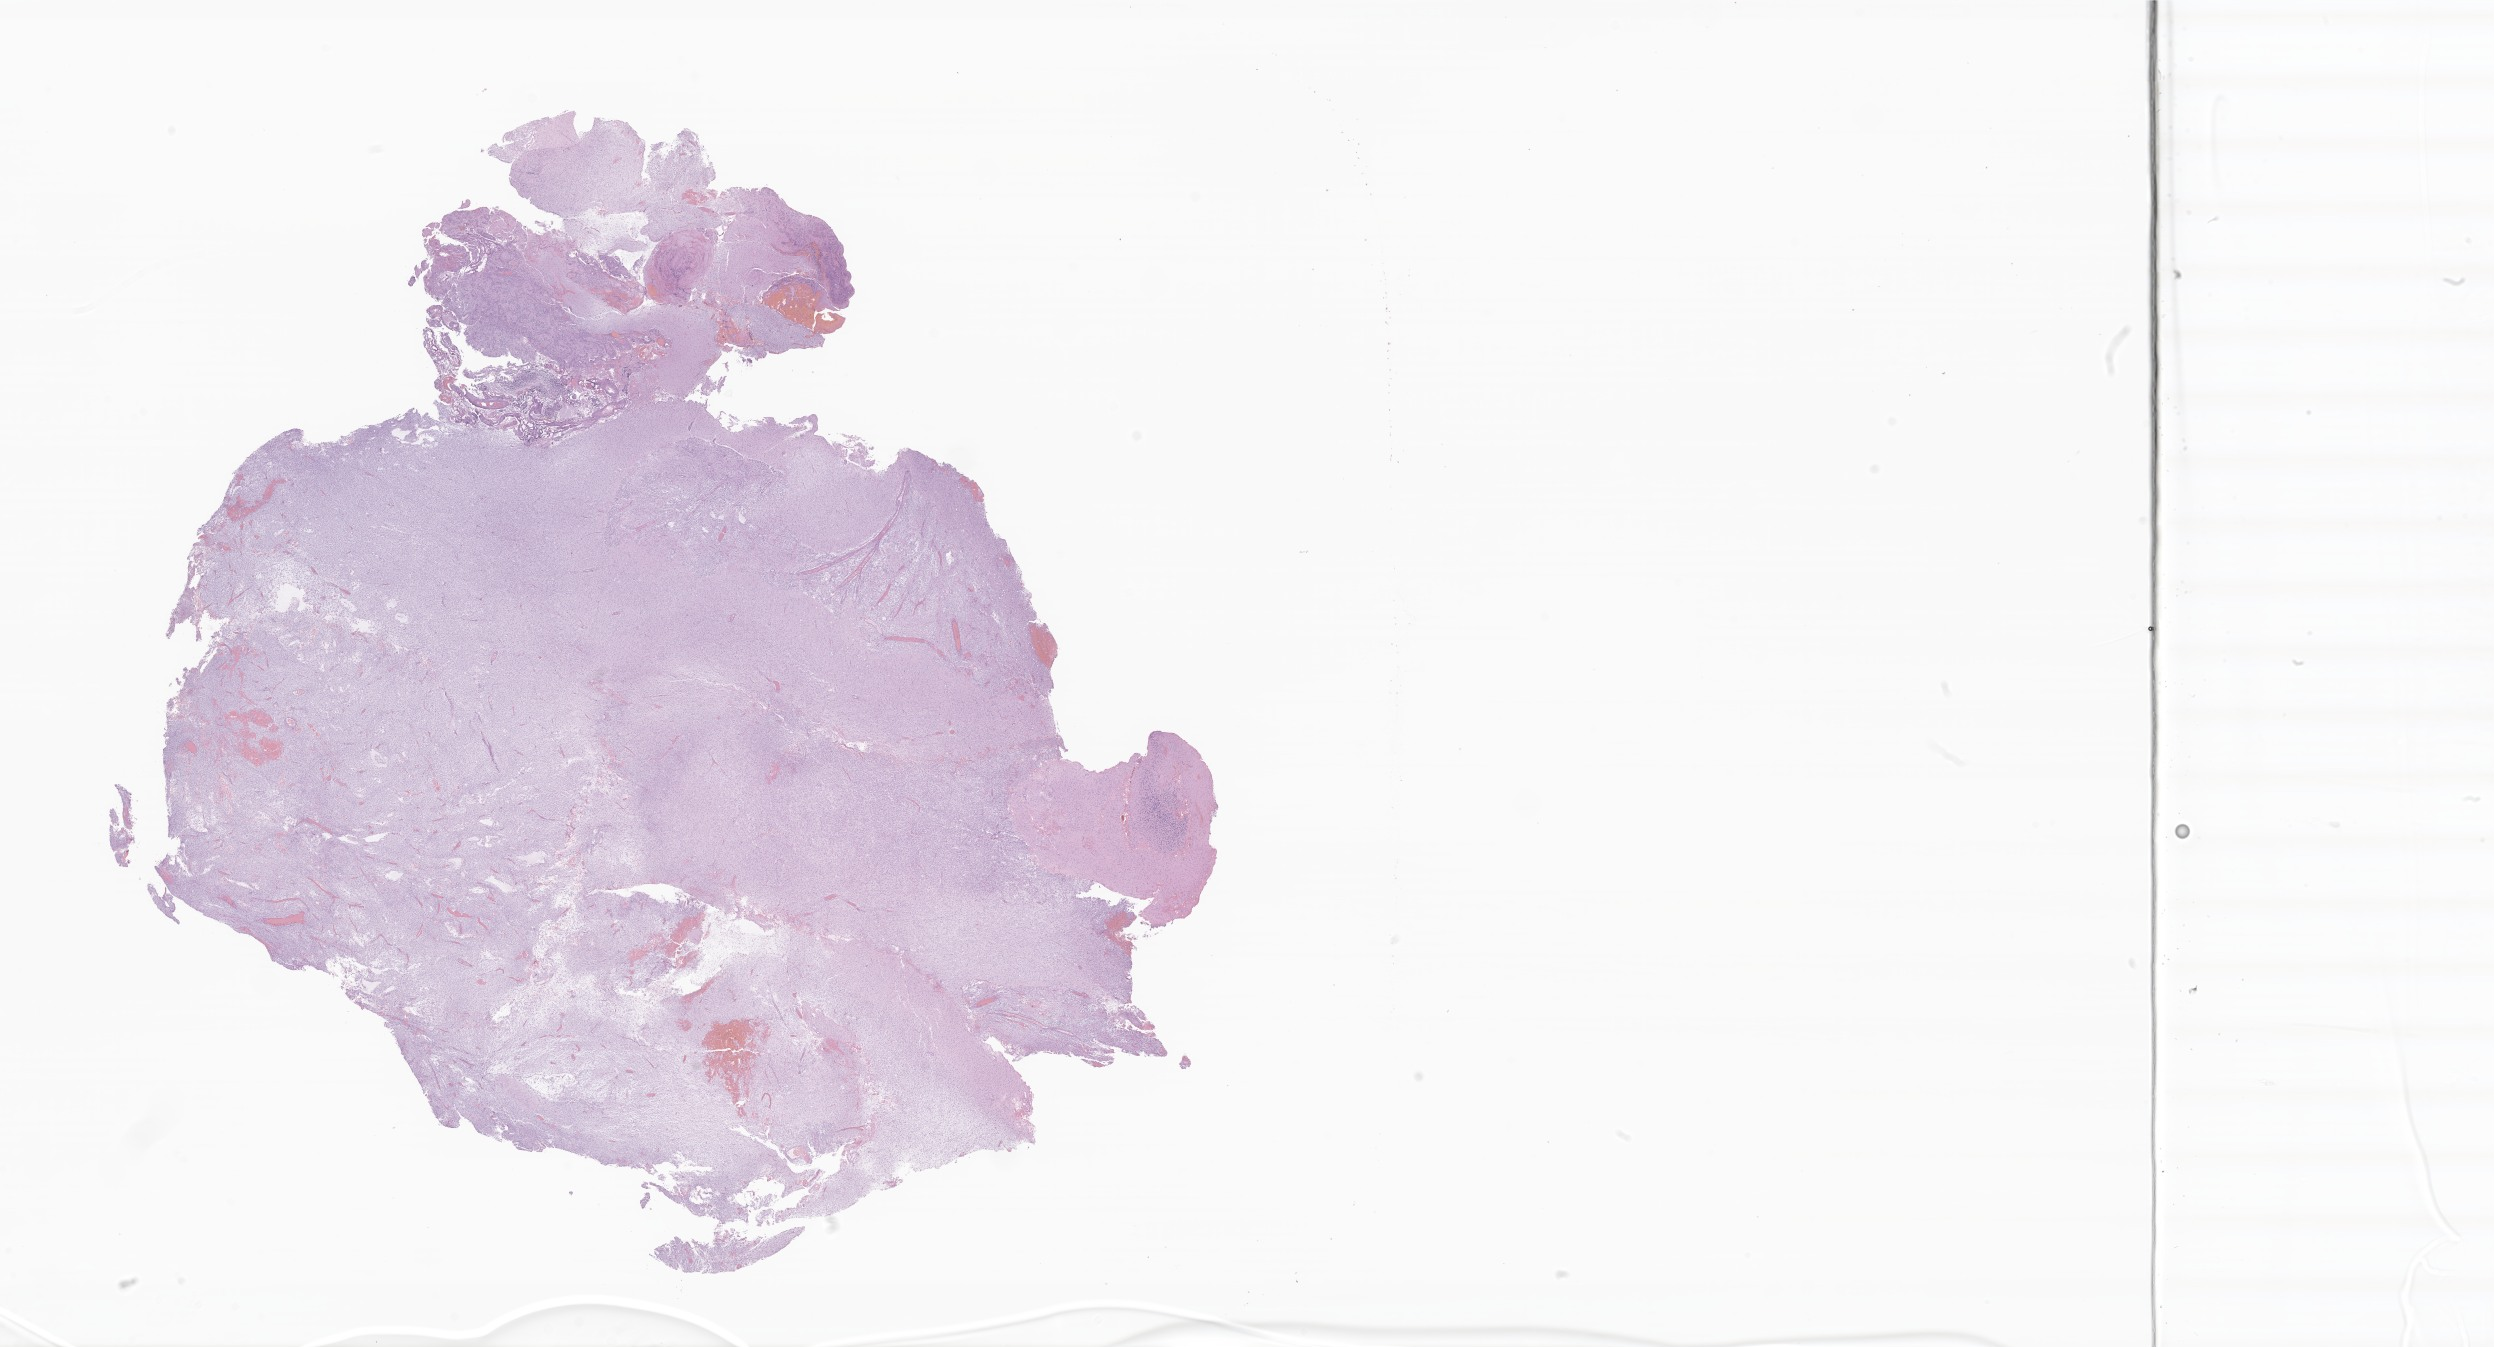
Hematoxylin and eosin (H&E) whole-slide image of tumor tissue from the cerebellum, shown as a low-resolution overview of the whole scanned area (about 42.1 x 22.7 mm); formalin-fixed paraffin-embedded section. Male patient, age 663 days (about 1.8 years).
Diagnosis: Pilocytic astrocytoma.